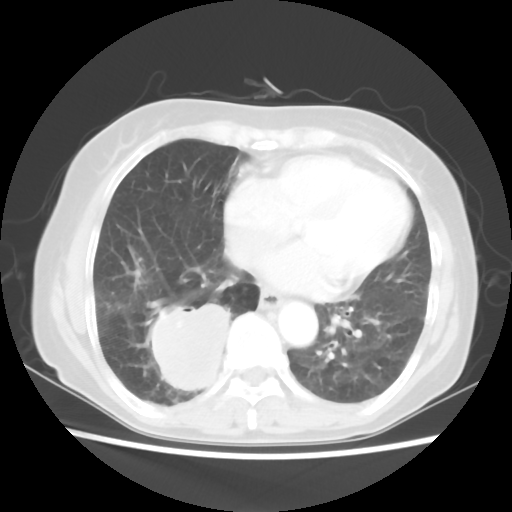
Chest CT, one axial slice; lung window (W 1500 / L -600 HU); 512 × 512 image matrix, field of view 332 × 332 mm. Female patient, age 66 years. From the clinical record (not read from this slice): clinical TNM (as recorded): T2 N3 M0; histopathological grade: G3.
Structures marked on this image (bounding box drawn by a radiologist):
- lung tumour (recorded histology: small cell carcinoma): bounding box <133,289,237,404> (left, top, right, bottom; pixels)